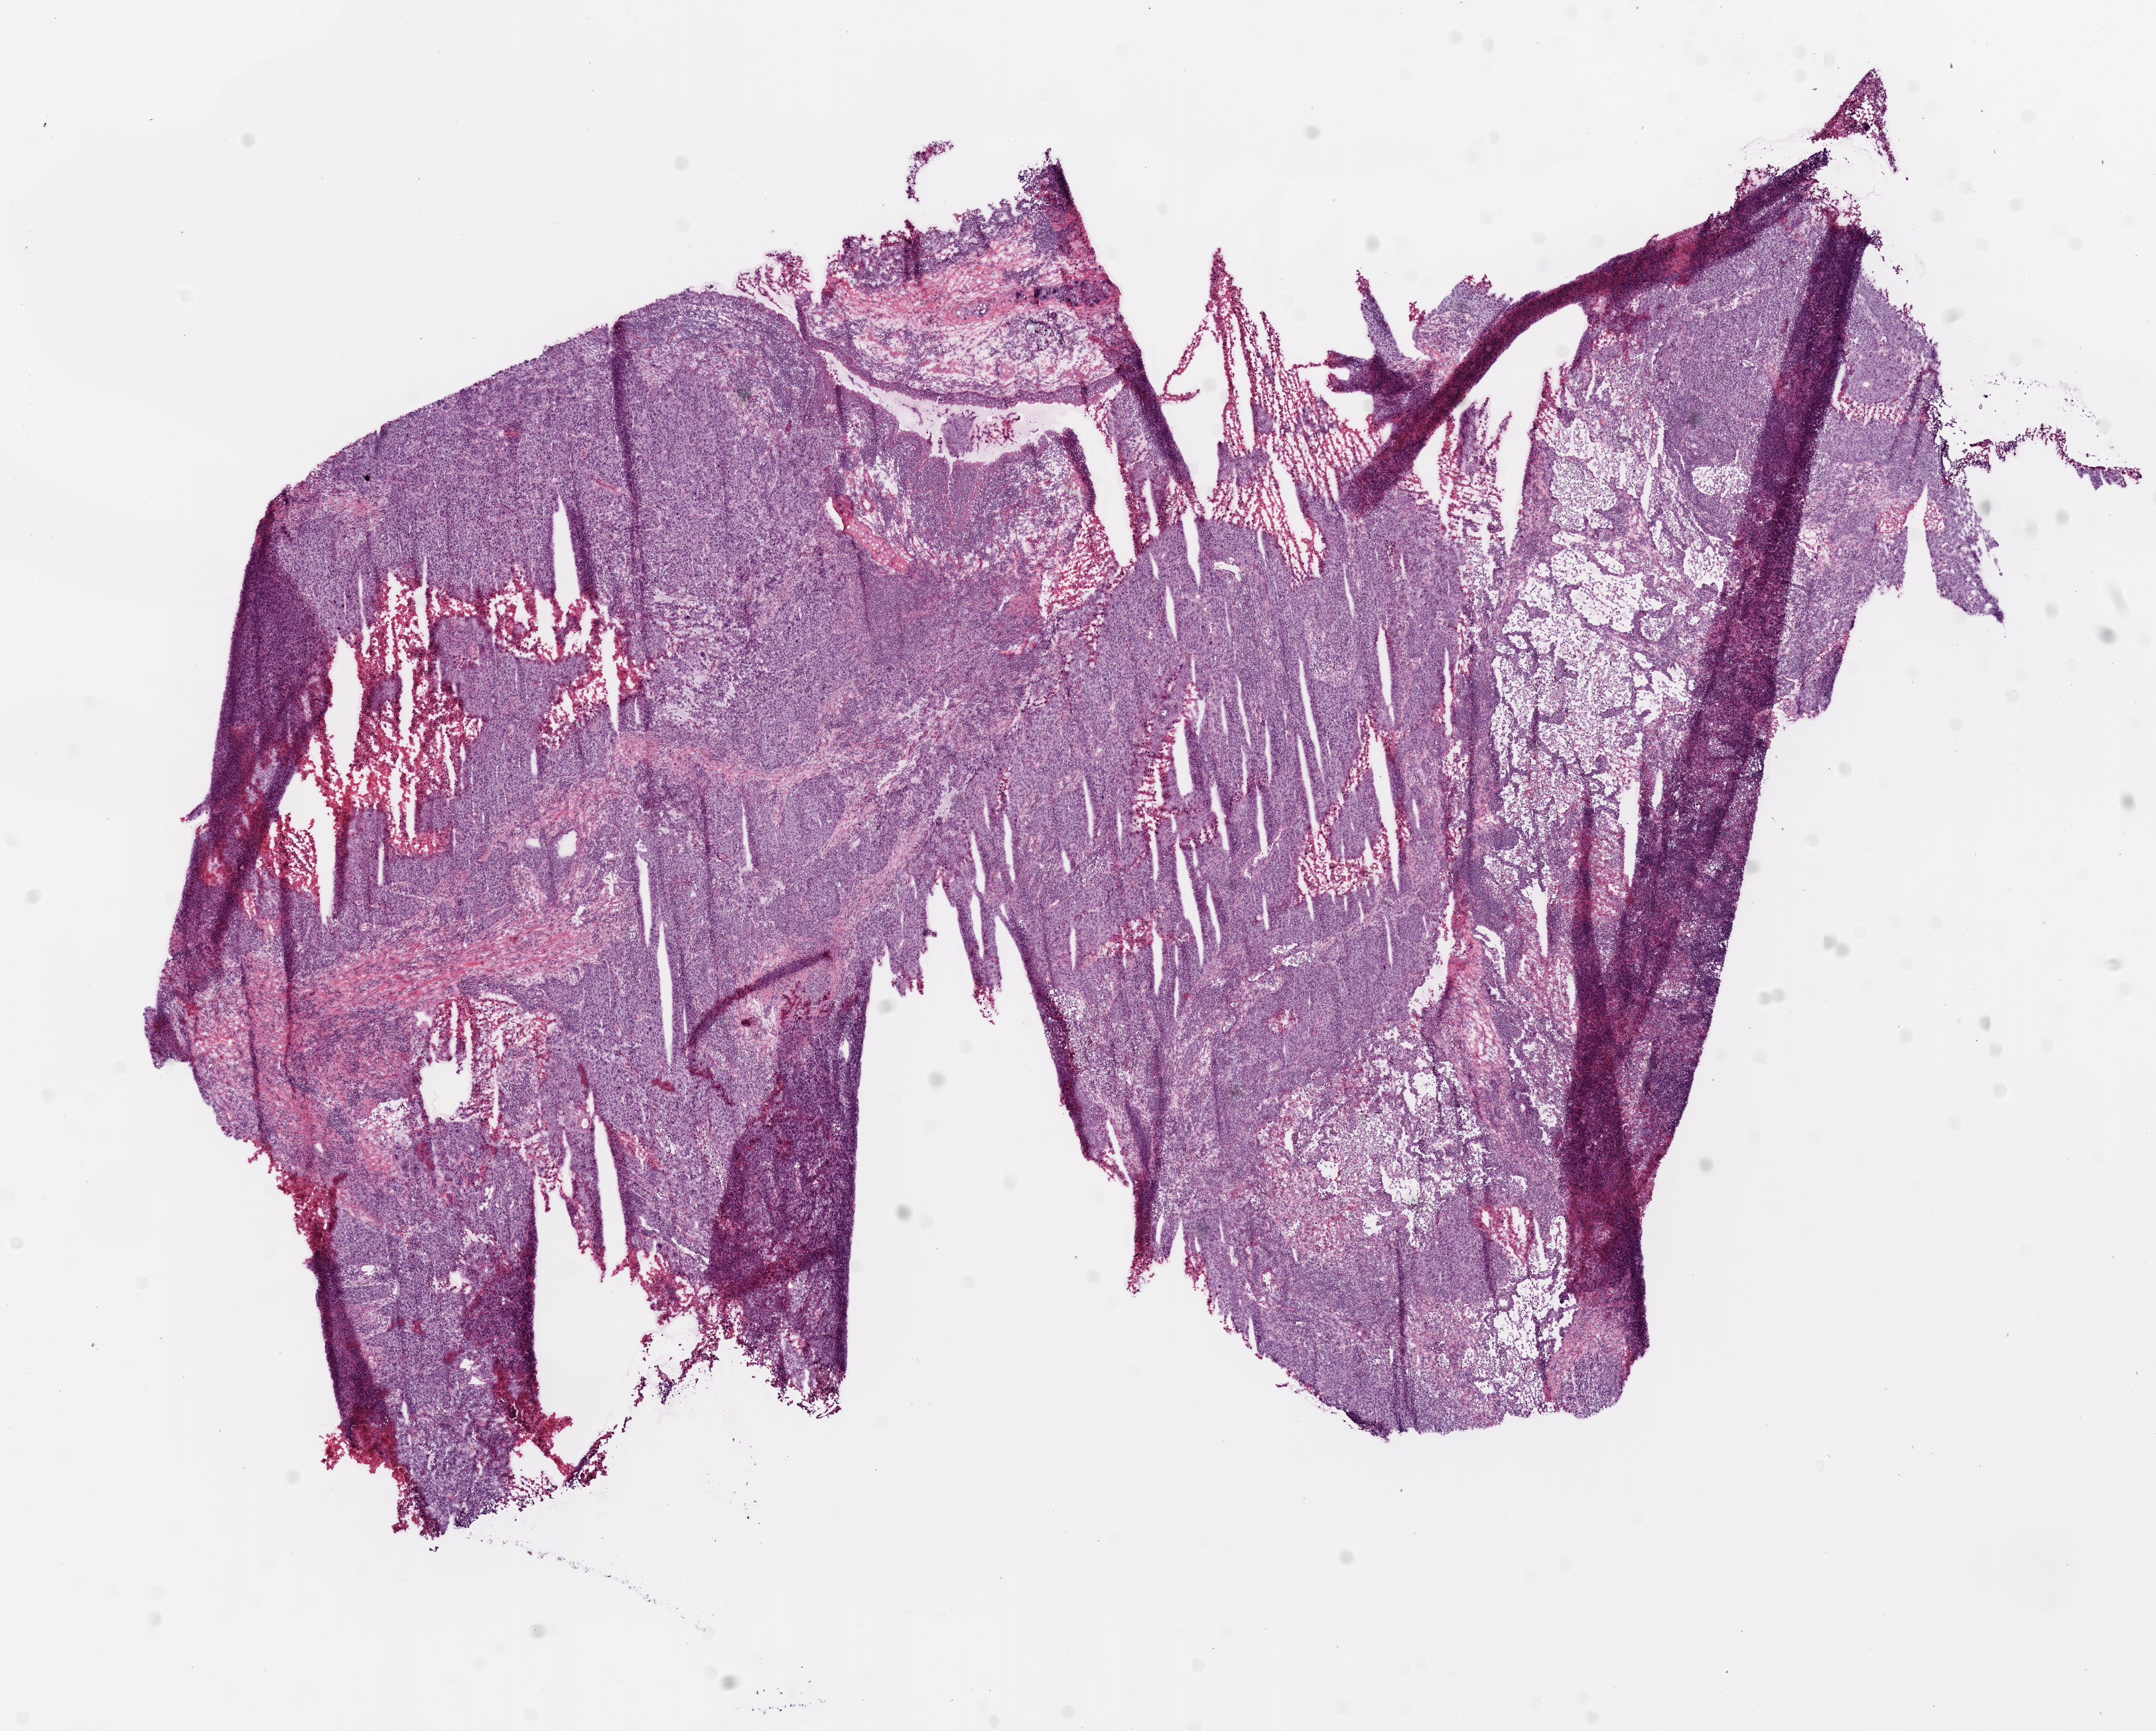
Digitized H&E tissue section (whole slide) — whole scanned area (about 13.0 x 10.5 mm, acquisition: 20x scan) shown as a low-resolution overview; frozen section from the bottom of the tissue portion; sample: primary tumour, lung. Patient: male, age at initial diagnosis 71 years. Slide review estimates, as recorded: tumour cells 60%, tumour nuclei 80%, normal cells 15%, stromal cells 5%, necrosis 20%.
• AJCC pathologic stage: IB (5th edition)
• pathologic diagnosis: Squamous cell carcinoma, NOS